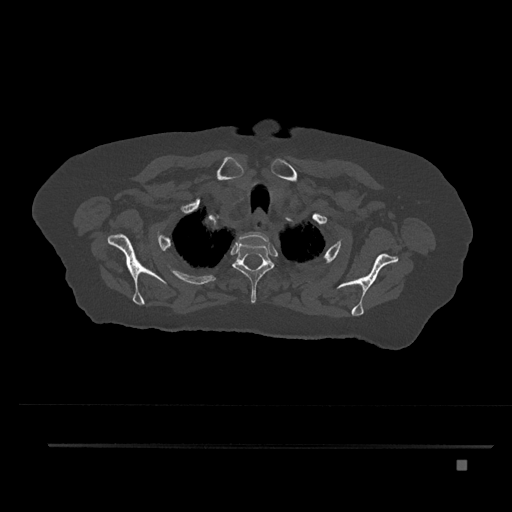
CT including the spine, one axial slice. Reconstruction kernel Br40s/3. Bone window (W 1800 / L 400 HU). 0.5 mm slice thickness. 512 × 512 image matrix, field of view 437 × 437 mm. Patient: female, 76 years. Case-level facts recorded for this patient, not image findings: primary cancer: lung; vertebrae with lytic lesions (as recorded): T11, L3.
Outlined on this slice (semi-automatically segmented with operator editing):
- T1 vertebra: bounding box (x1, y1, x2, y2) in pixels: (239, 232, 269, 248)
- T2 vertebra: (232, 241, 275, 303)